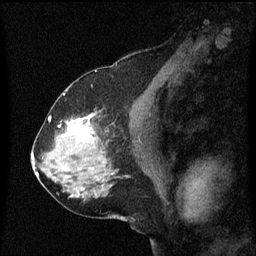
Breast MRI (dynamic contrast-enhanced), one sagittal slice. Slice 34 of 60 in the series (ordered by position). Dynamic contrast-enhanced series, image 2 of 3 at this slice position (ordered by acquisition). 1.5 T. TE 4.2 ms, TR 8.4 ms. 2 mm slice thickness. 256 × 256 image matrix, field of view 200 × 200 mm. Female patient, age 58 years.
Annotated regions visible in this slice (semi-automatically segmented with operator editing):
- analysis volume of interest (the breast-tissue region the enhancement analysis was run in; not a lesion): box from (x=58, y=114) to (x=99, y=151) px
- tumour enhancement mask (voxels above the 70 % enhancement threshold inside the analysis volume of interest): (x=62, y=114)–(x=95, y=141)